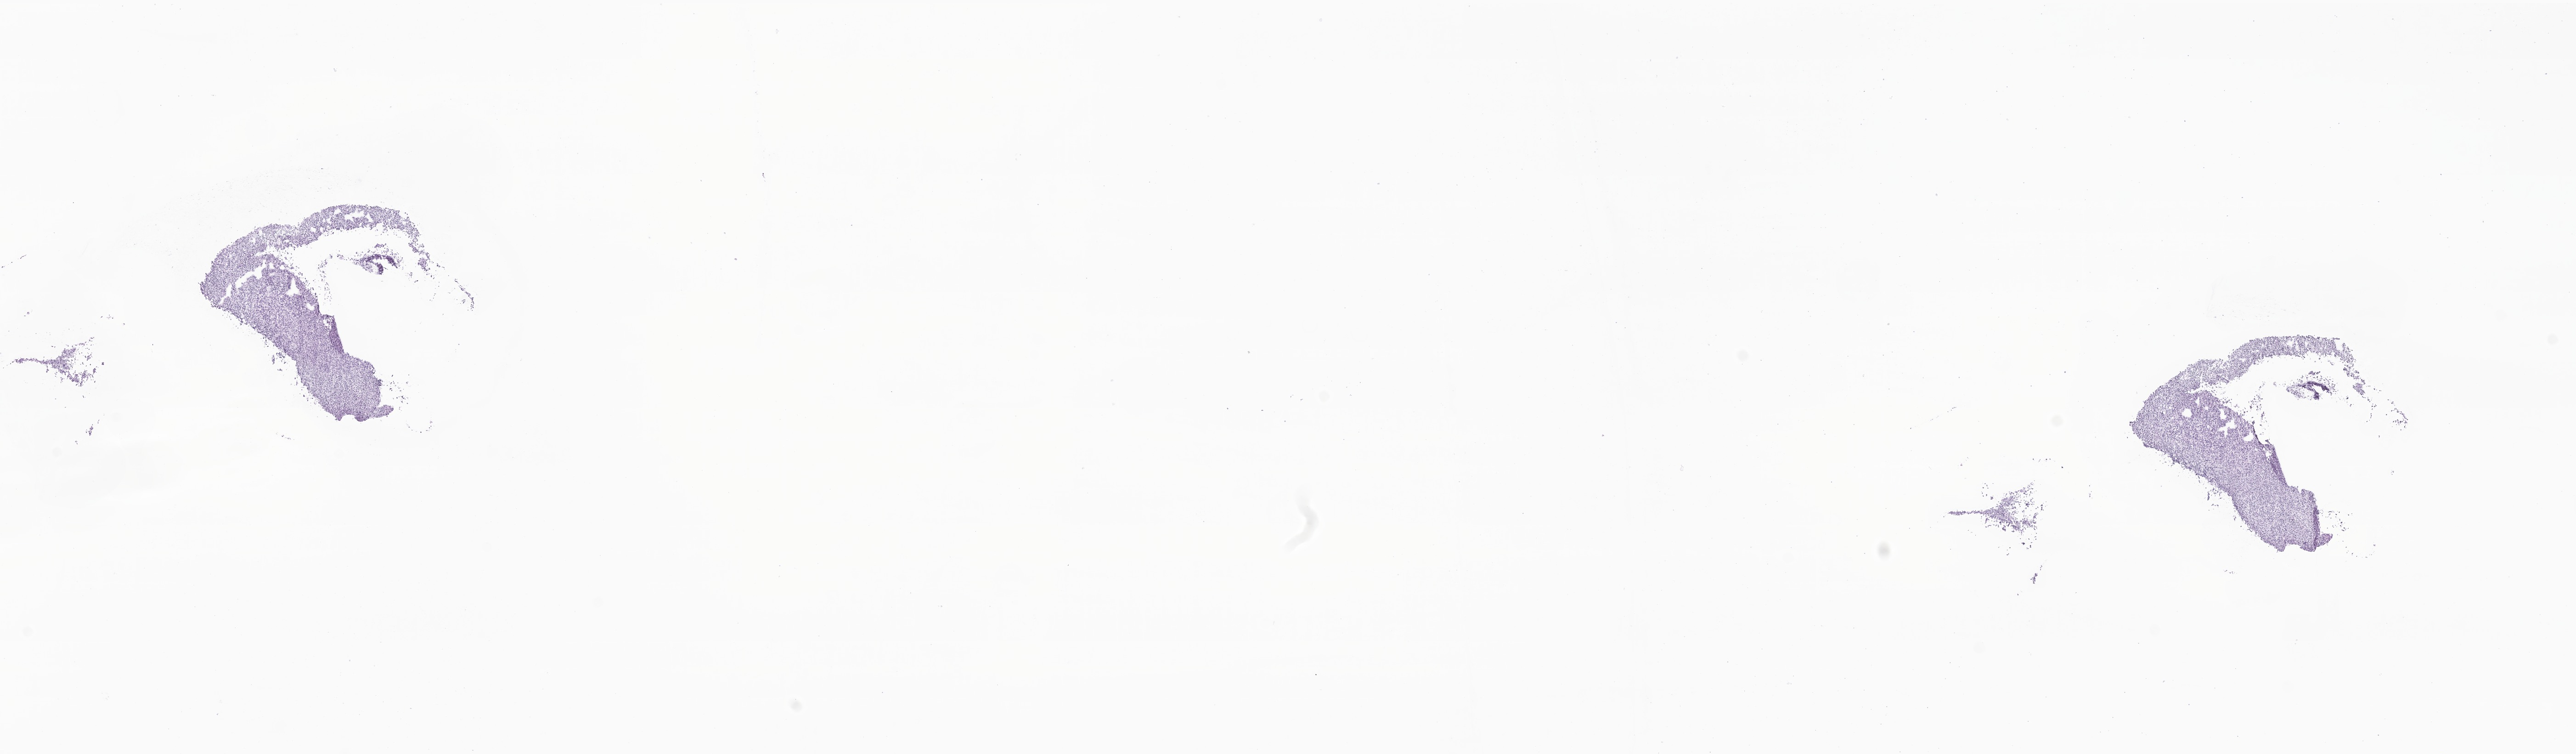
Haematoxylin and eosin whole-slide image of tumor tissue from the brain — shown as a low-resolution overview of the whole scanned area (about 23.6 x 6.9 mm); frozen section. Male patient, age 66 months (5 years 6 months).
- diagnosis (ICD-O-3 morphology term): Medulloblastoma, NOS